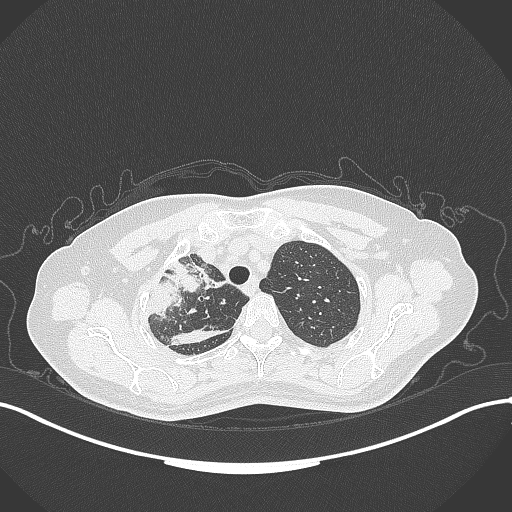
Chest CT, one axial slice. Position 263 of 309 along the scan axis. Reconstruction kernel B70f. Lung window (W 1500 / L -600 HU). 1 mm slice thickness. 512 × 512 image matrix, field of view 400 × 400 mm. Female patient, age 60 years. Case-level facts recorded for this patient, not image findings: clinical TNM (as recorded): T3 N1 M1.
Structures marked on this image (bounding box drawn by a radiologist):
- lung tumour (recorded histology: adenocarcinoma): bounding box [x1, y1, x2, y2] px = [138, 261, 230, 316]